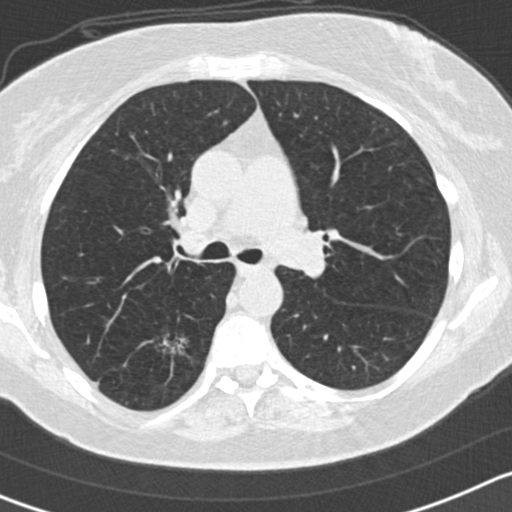
Chest CT (low-dose screening protocol), one axial image. First (baseline) screen. Lung window (W 1500 / L -600 HU). Standard (soft-tissue) reconstruction kernel (B30f). 120 kVp. Female participant, aged 65 years at enrolment. Former smoker at enrolment.
Expert reader's lesion annotation, bounding box (x1, y1, x2, y2) in pixels: (134, 316, 199, 379). Reader record for this screening exam (exam-level; its link to the box is not recorded): non-calcified nodule or mass ≥4 mm, right lower lobe, 14 × 13 mm, spiculated (stellate) margins, mixed attenuation. Later outcome: lung cancer diagnosed 565 days after this screen — adenocarcinoma, NOS, right lower lobe, moderately differentiated (G2), stage IA (AJCC 6th edition), 25 mm at pathology.